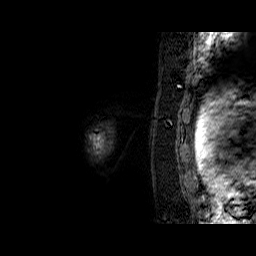
Breast MRI (dynamic contrast-enhanced), one sagittal slice. Slice 58 of 60 in the series (ordered by position). Dynamic contrast-enhanced series, time point 2 of 6 at this slice position (early post-contrast). 1.5 T. TE 6.3 ms, TR 32.9 ms. 4 mm slice thickness. 256 × 256 image matrix, field of view 200 × 200 mm. Female patient. Case-level facts recorded for this patient, not image findings: setting: breast cancer imaged before/during neoadjuvant chemotherapy; receptor status: triple-negative.
Structures marked on this image (semi-automatically segmented with operator editing):
- analysis volume of interest (the breast-tissue region the enhancement analysis was run in; not a lesion): bounding box [x1, y1, x2, y2] px = [92, 129, 110, 153]
- tumour enhancement mask (voxels above the 100 % enhancement threshold inside the analysis volume of interest): [93, 134, 103, 149]